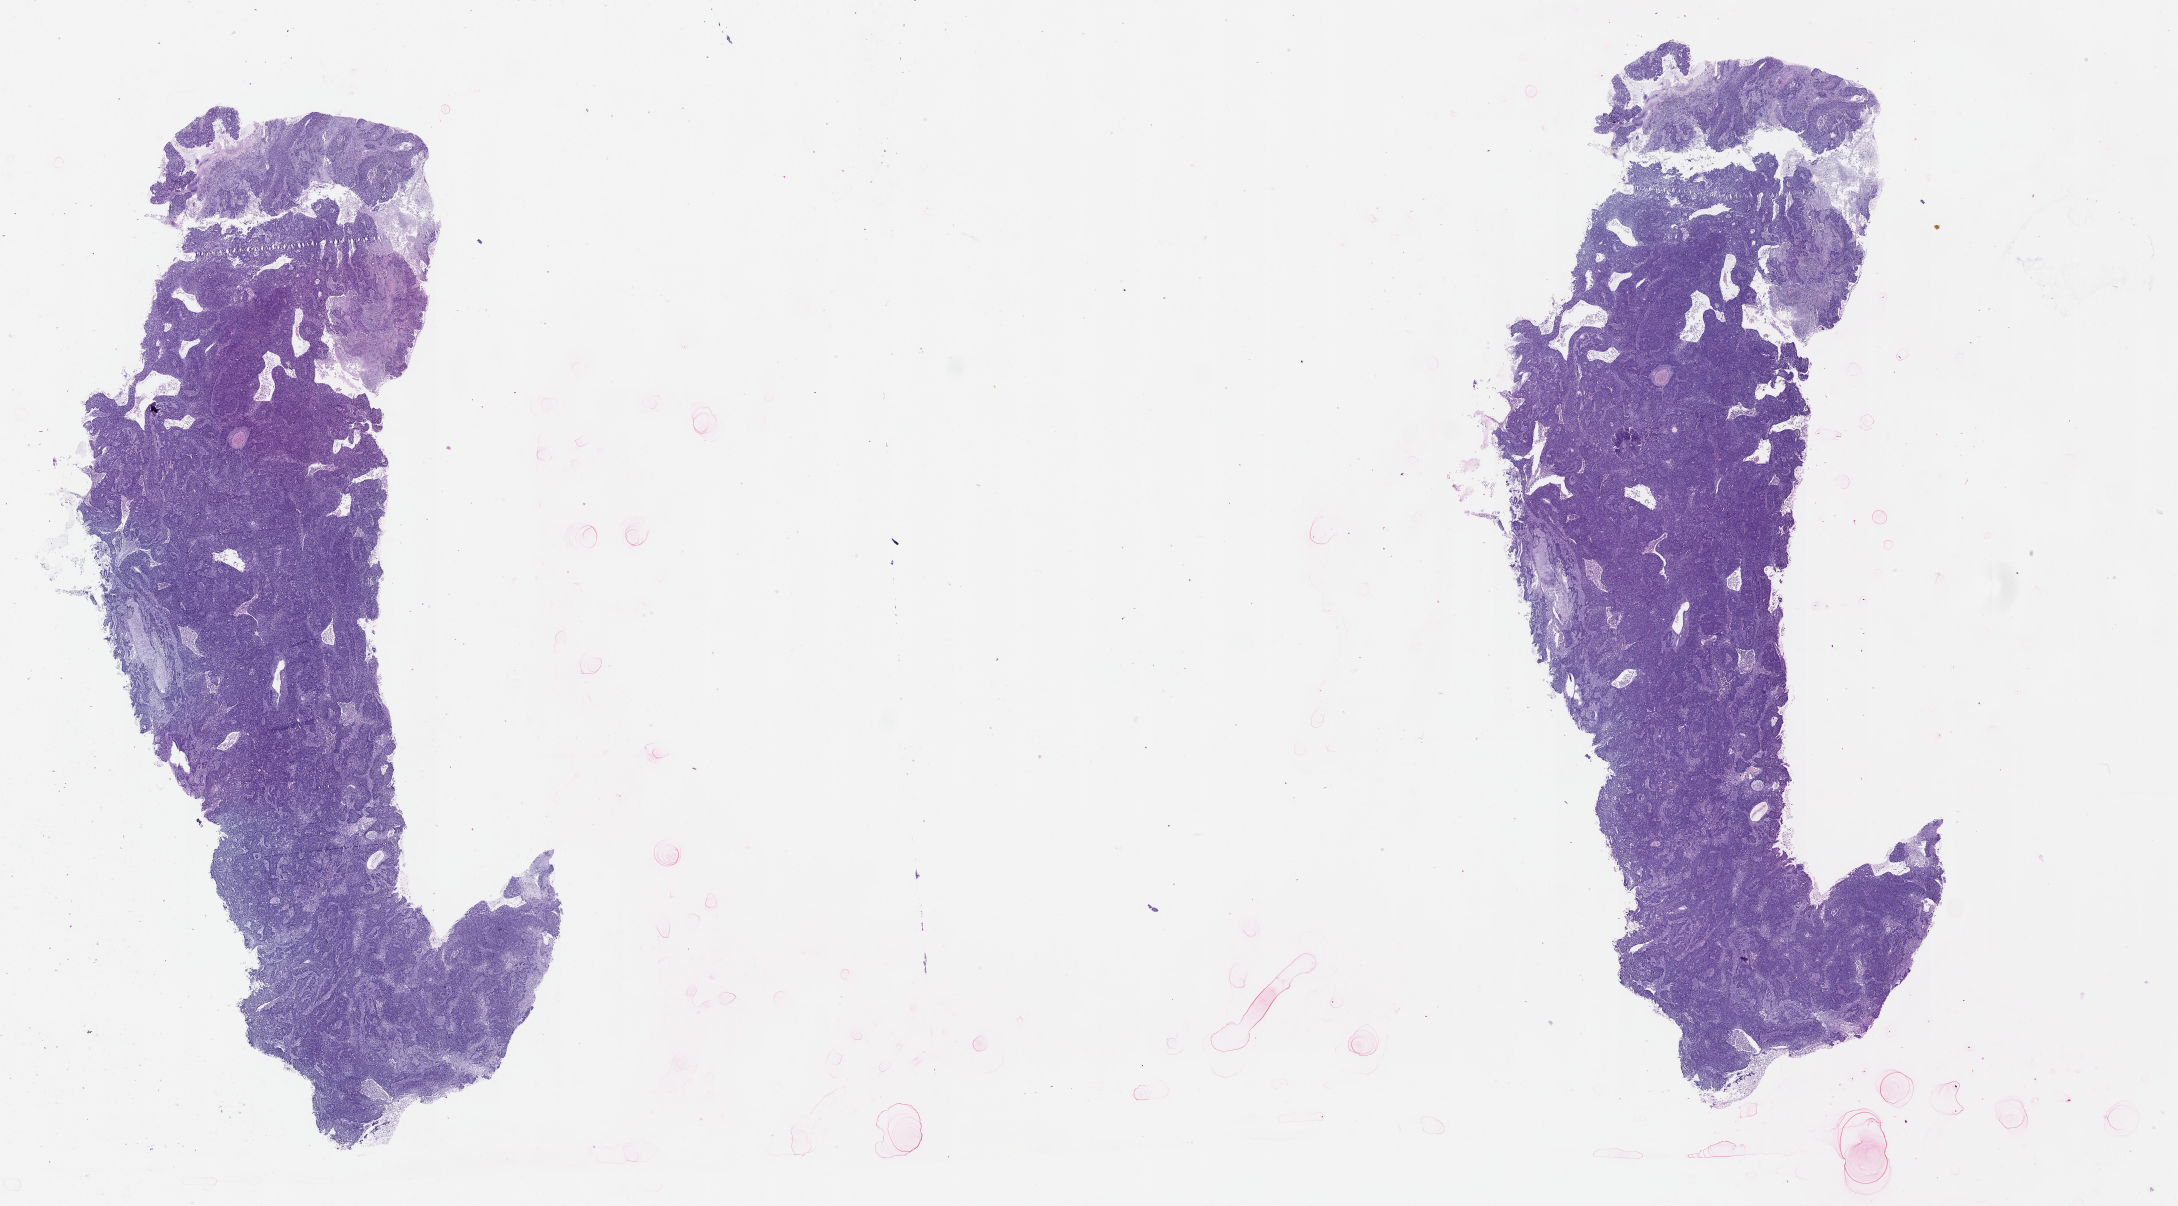
Digitized H&E tissue section (whole slide) — shown as a low-resolution overview of the whole scanned area (about 35.1 x 19.4 mm, slide scanned at 20x). Lung, tumour tissue. 62-year-old female patient.
Patient diagnosis (cohort enrolment): squamous cell carcinoma (lung).